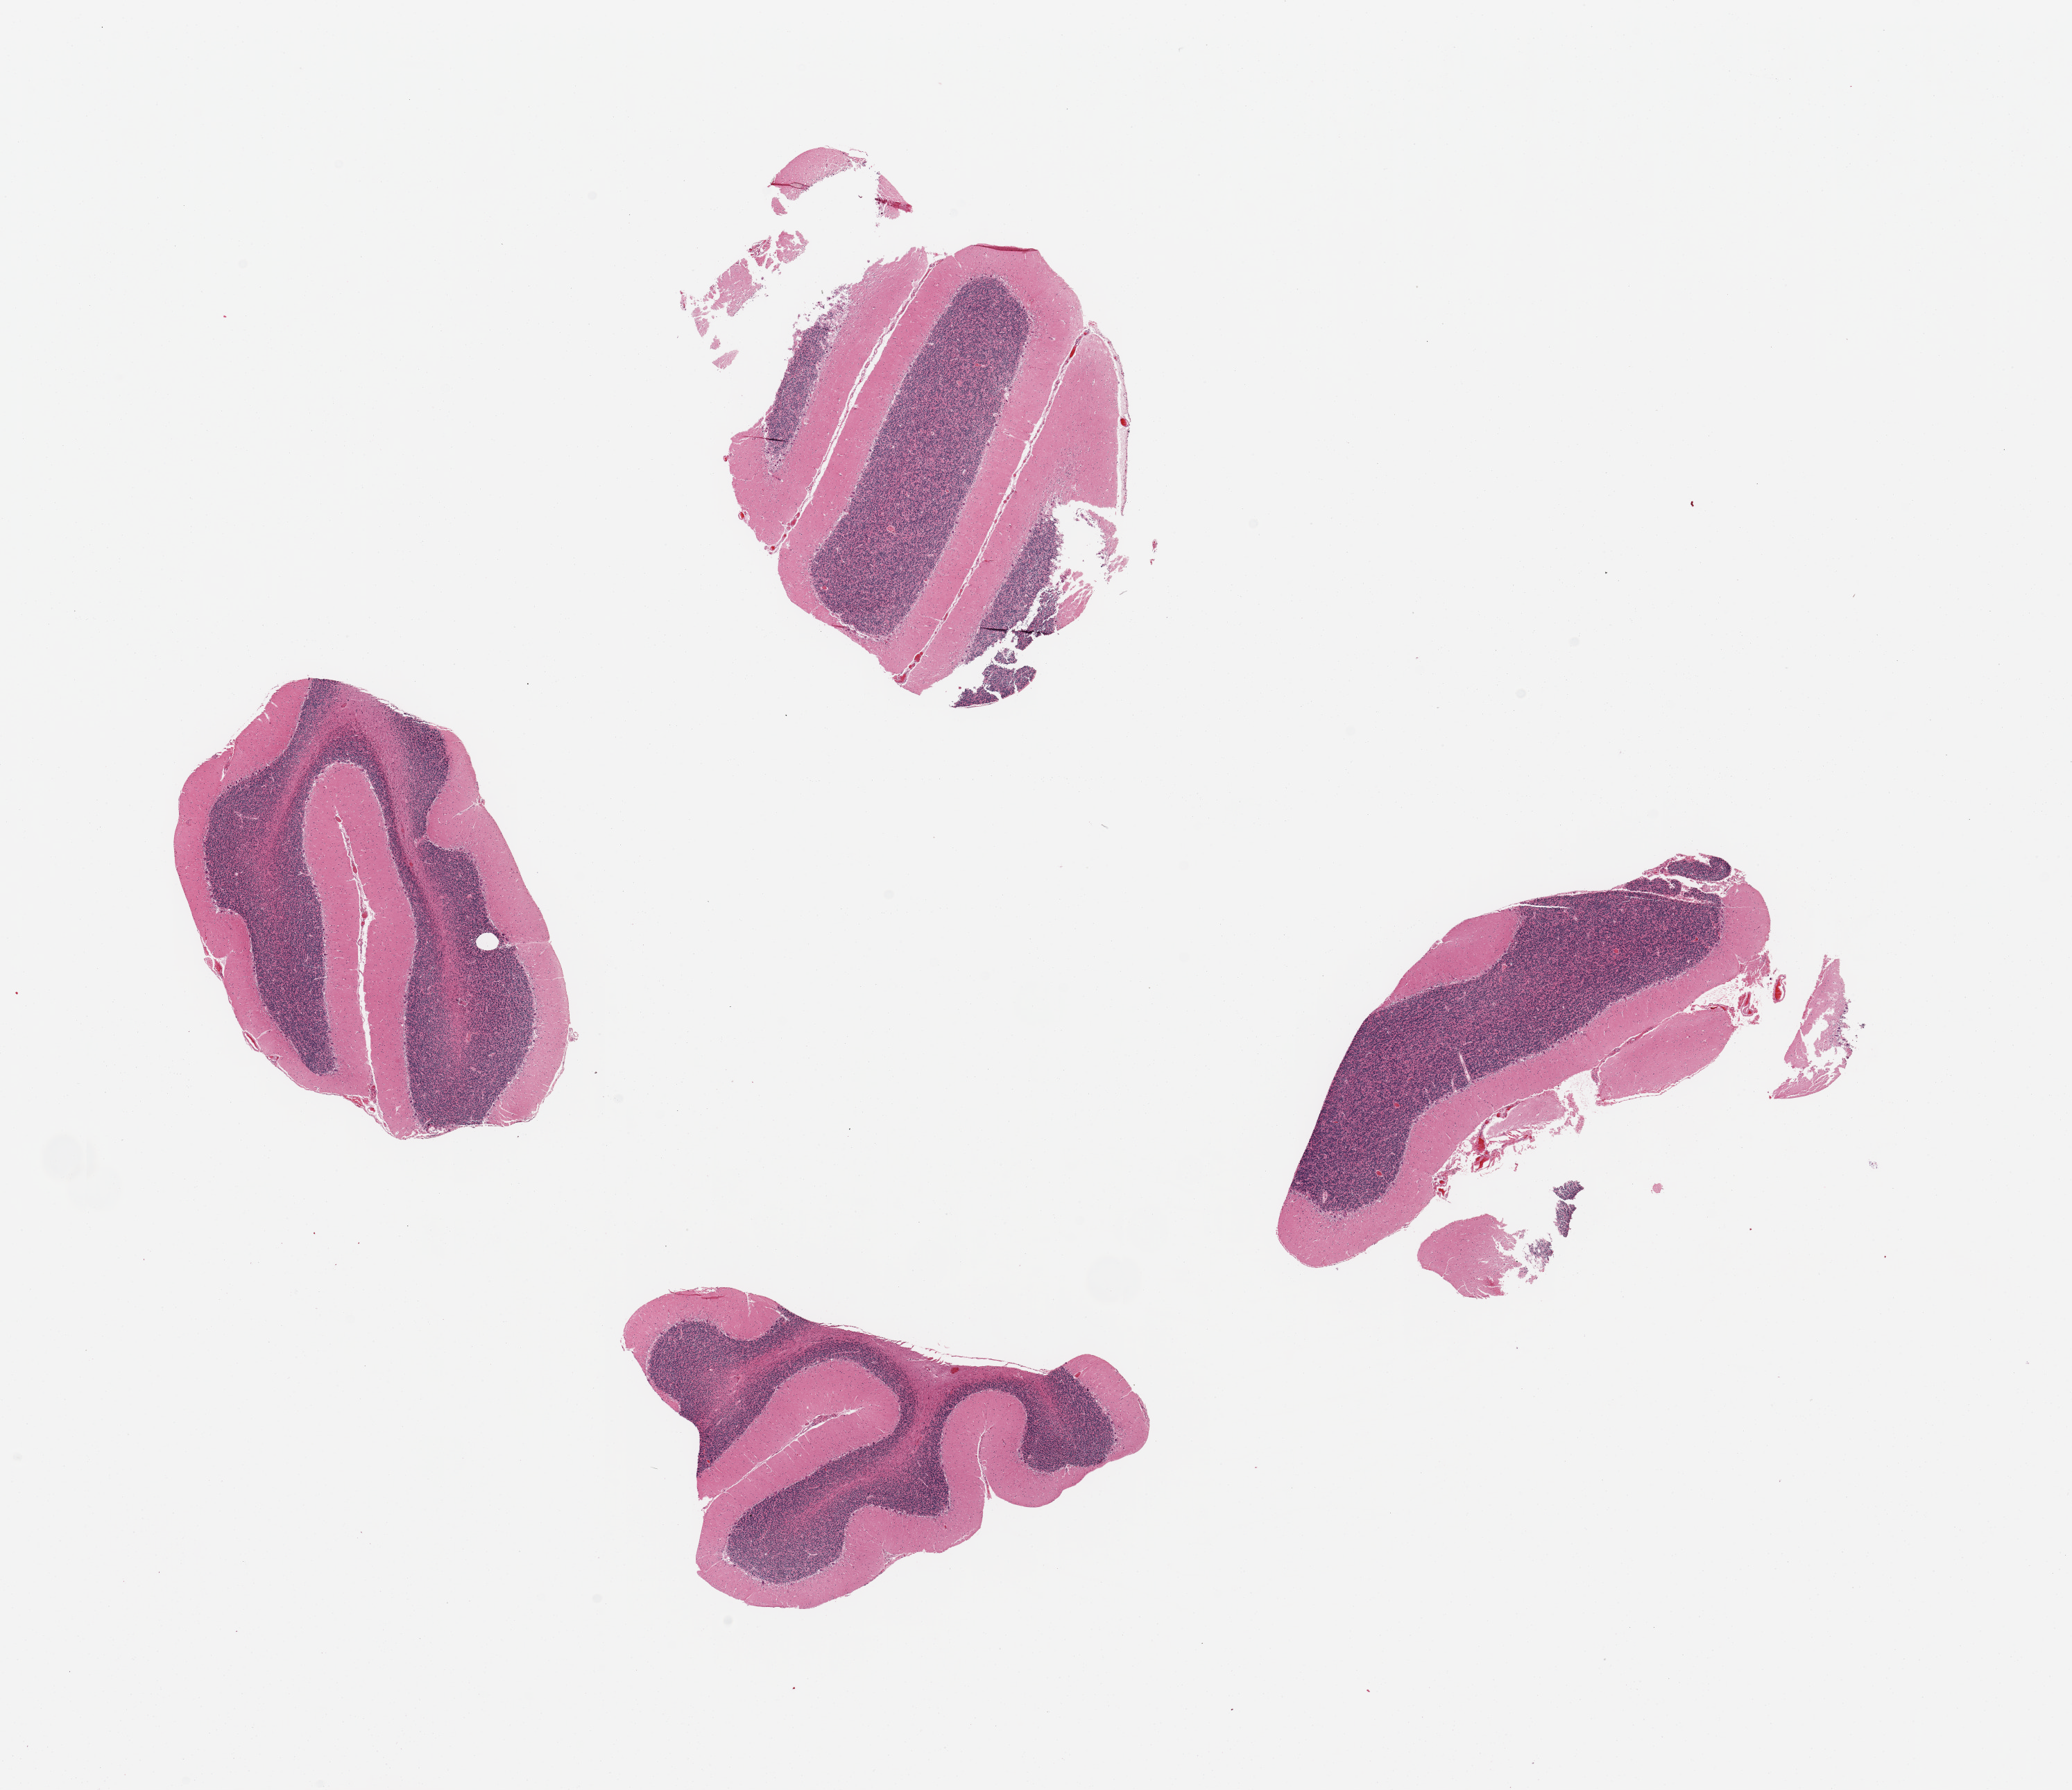
Whole-slide image, hematoxylin and eosin (H&E) stain, brightfield, whole scanned area (about 23.6 x 20.4 mm) shown as a low-resolution overview, PAXgene-fixed, paraffin-embedded tissue, section of cerebellum (target tissue), donor tissue sample. Female donor.
* review note (as recorded): 4 pieces, no evidence of hypoxic damage